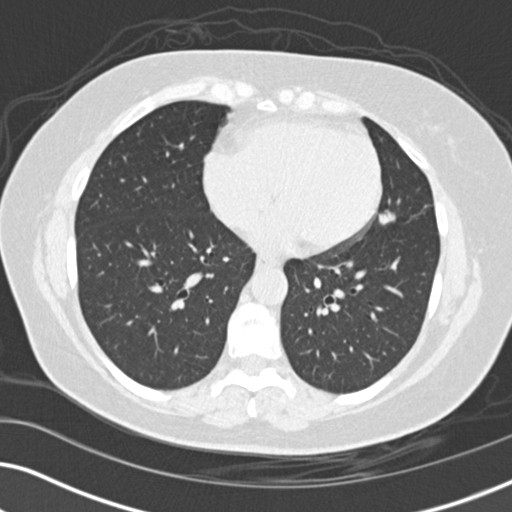
Low-dose screening chest CT, one axial slice. Position 65 of 152 along the scan axis. Reconstruction kernel B30f. 120 kVp. Lung window (W 1500 / L -600 HU). 512 × 512 image matrix, field of view 330 × 330 mm.
Annotated regions visible in this slice (manually delineated by an expert):
- lesion 1 (tumor, upper lobe of left lung): bounding box <379,209,396,225> (left, top, right, bottom; pixels)